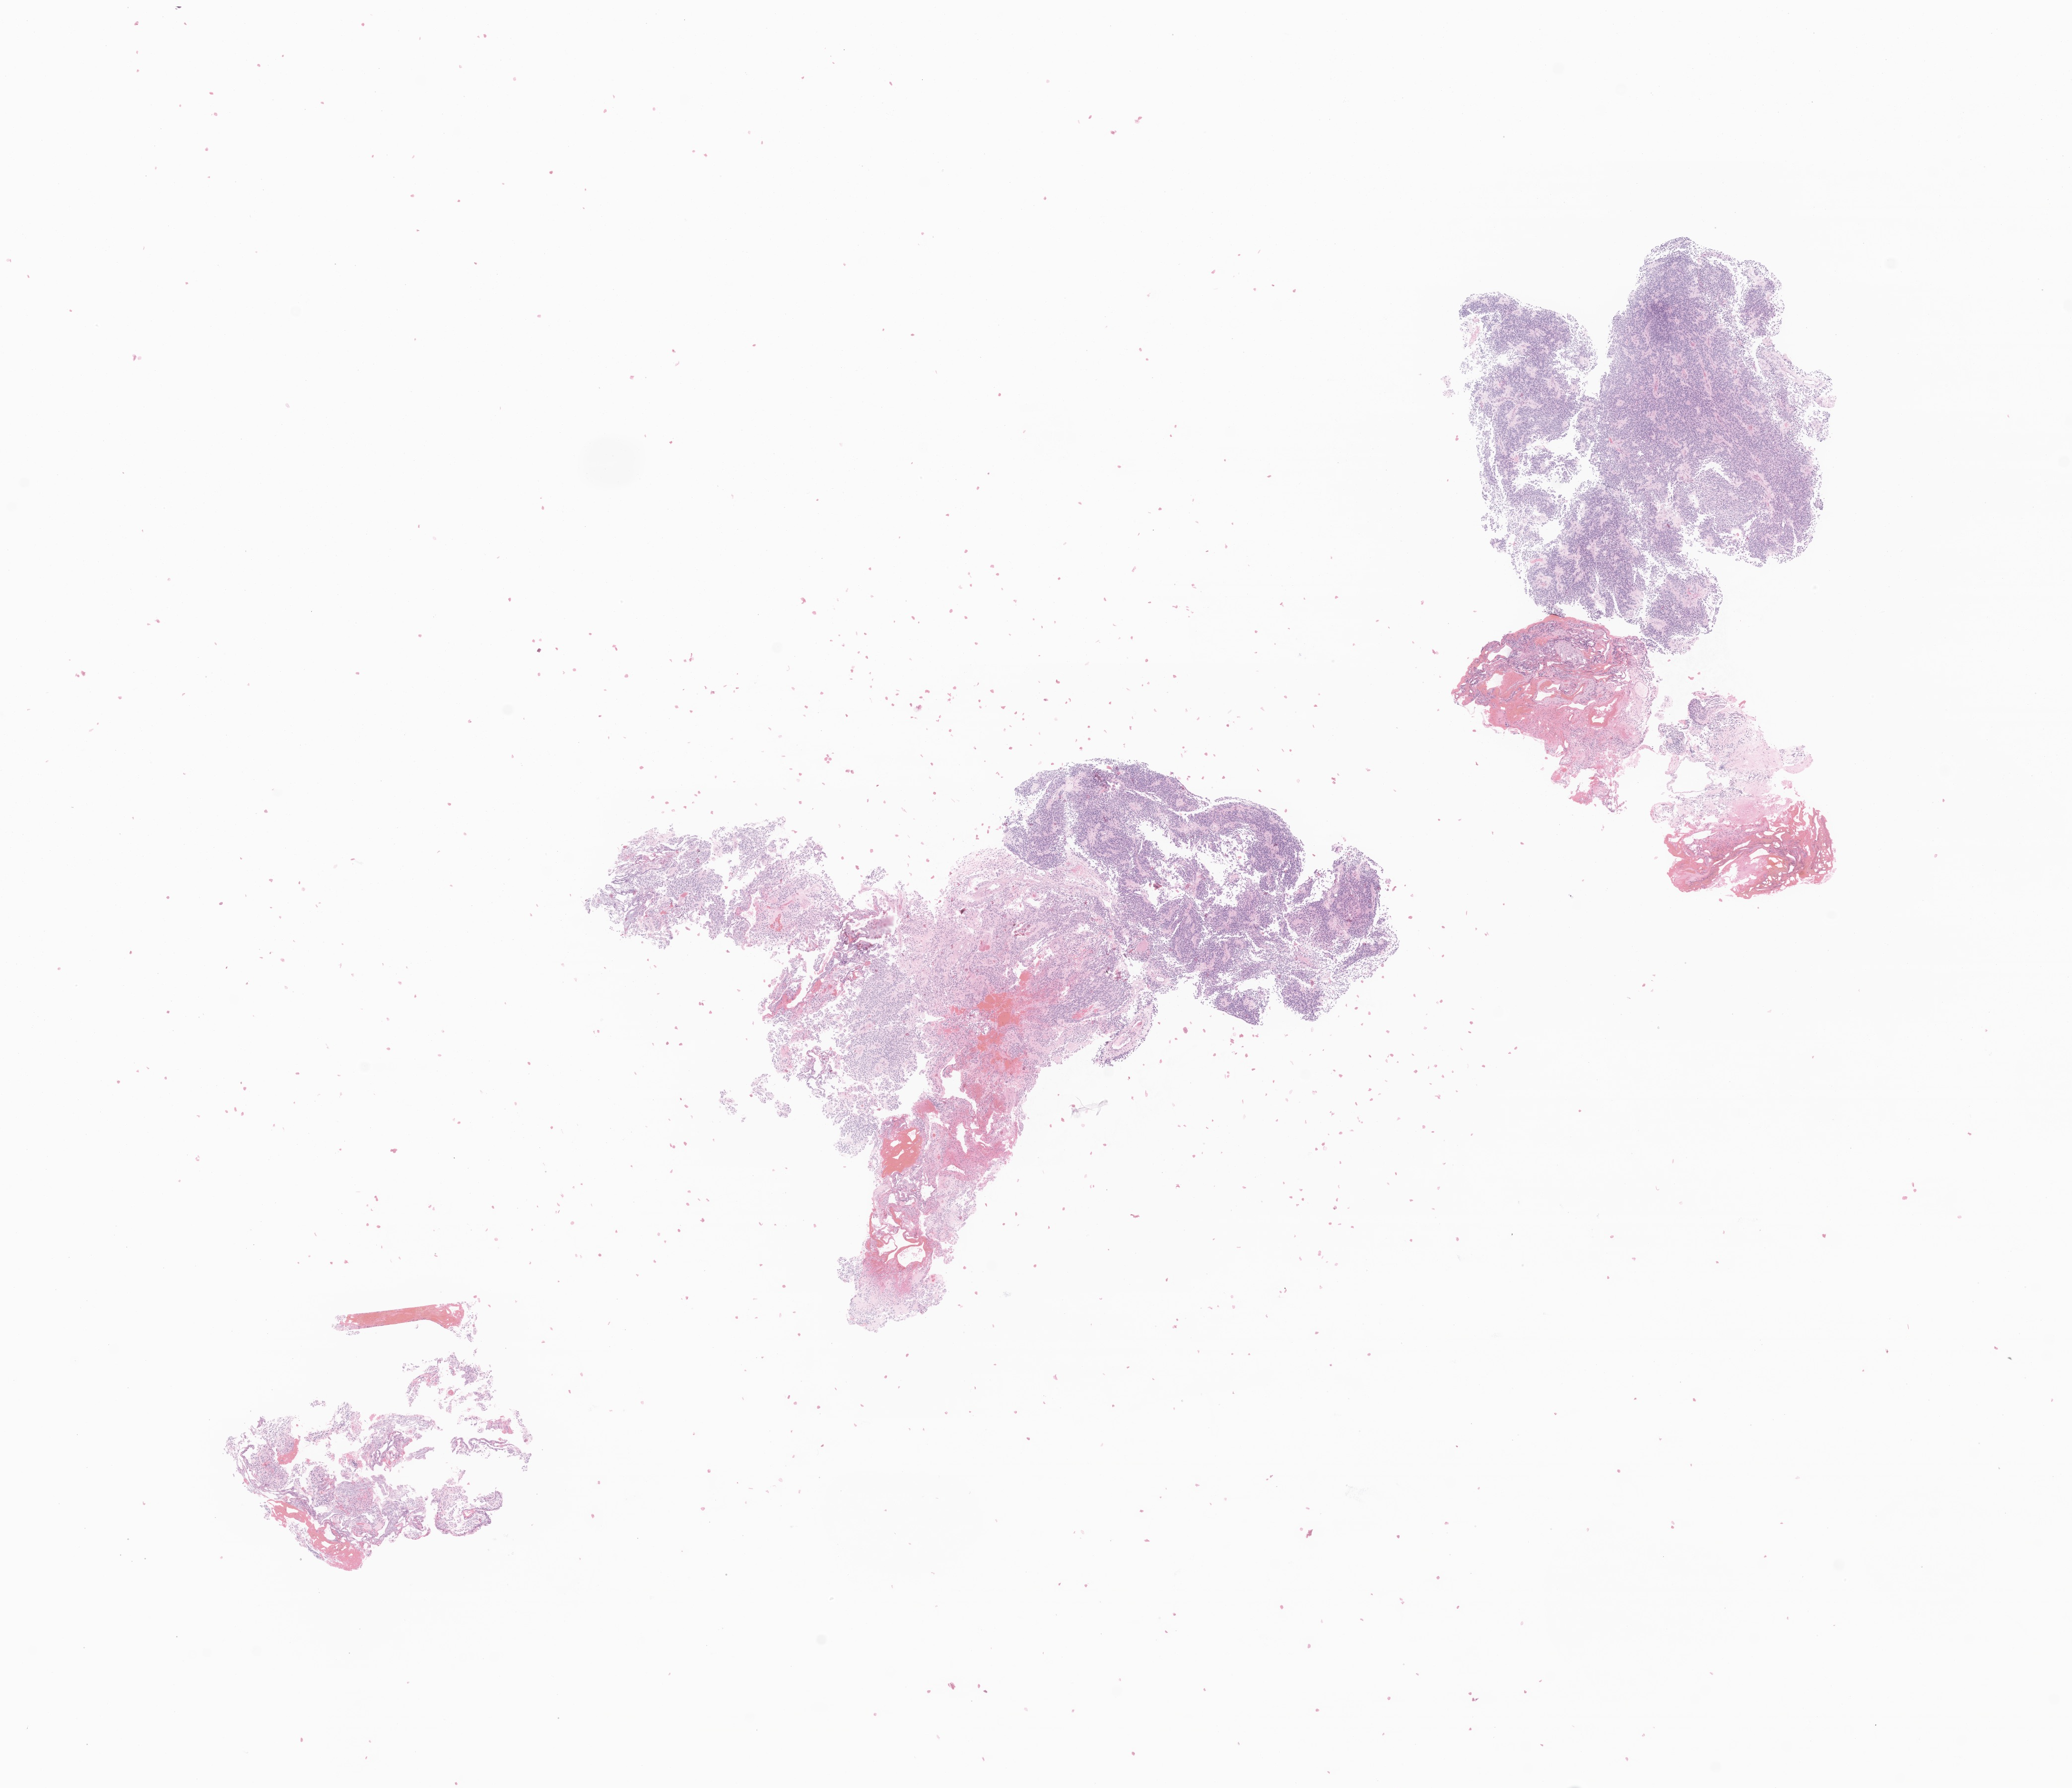
Whole-slide image, haematoxylin and eosin stain of tumor tissue from the brain — shown as a low-resolution overview of the whole scanned area (about 17.6 x 15.2 mm). Formalin-fixed, paraffin-embedded (FFPE) tissue. Patient female; age 214 months (17 years 10 months).
Recorded diagnosis: Ependymoma, NOS.